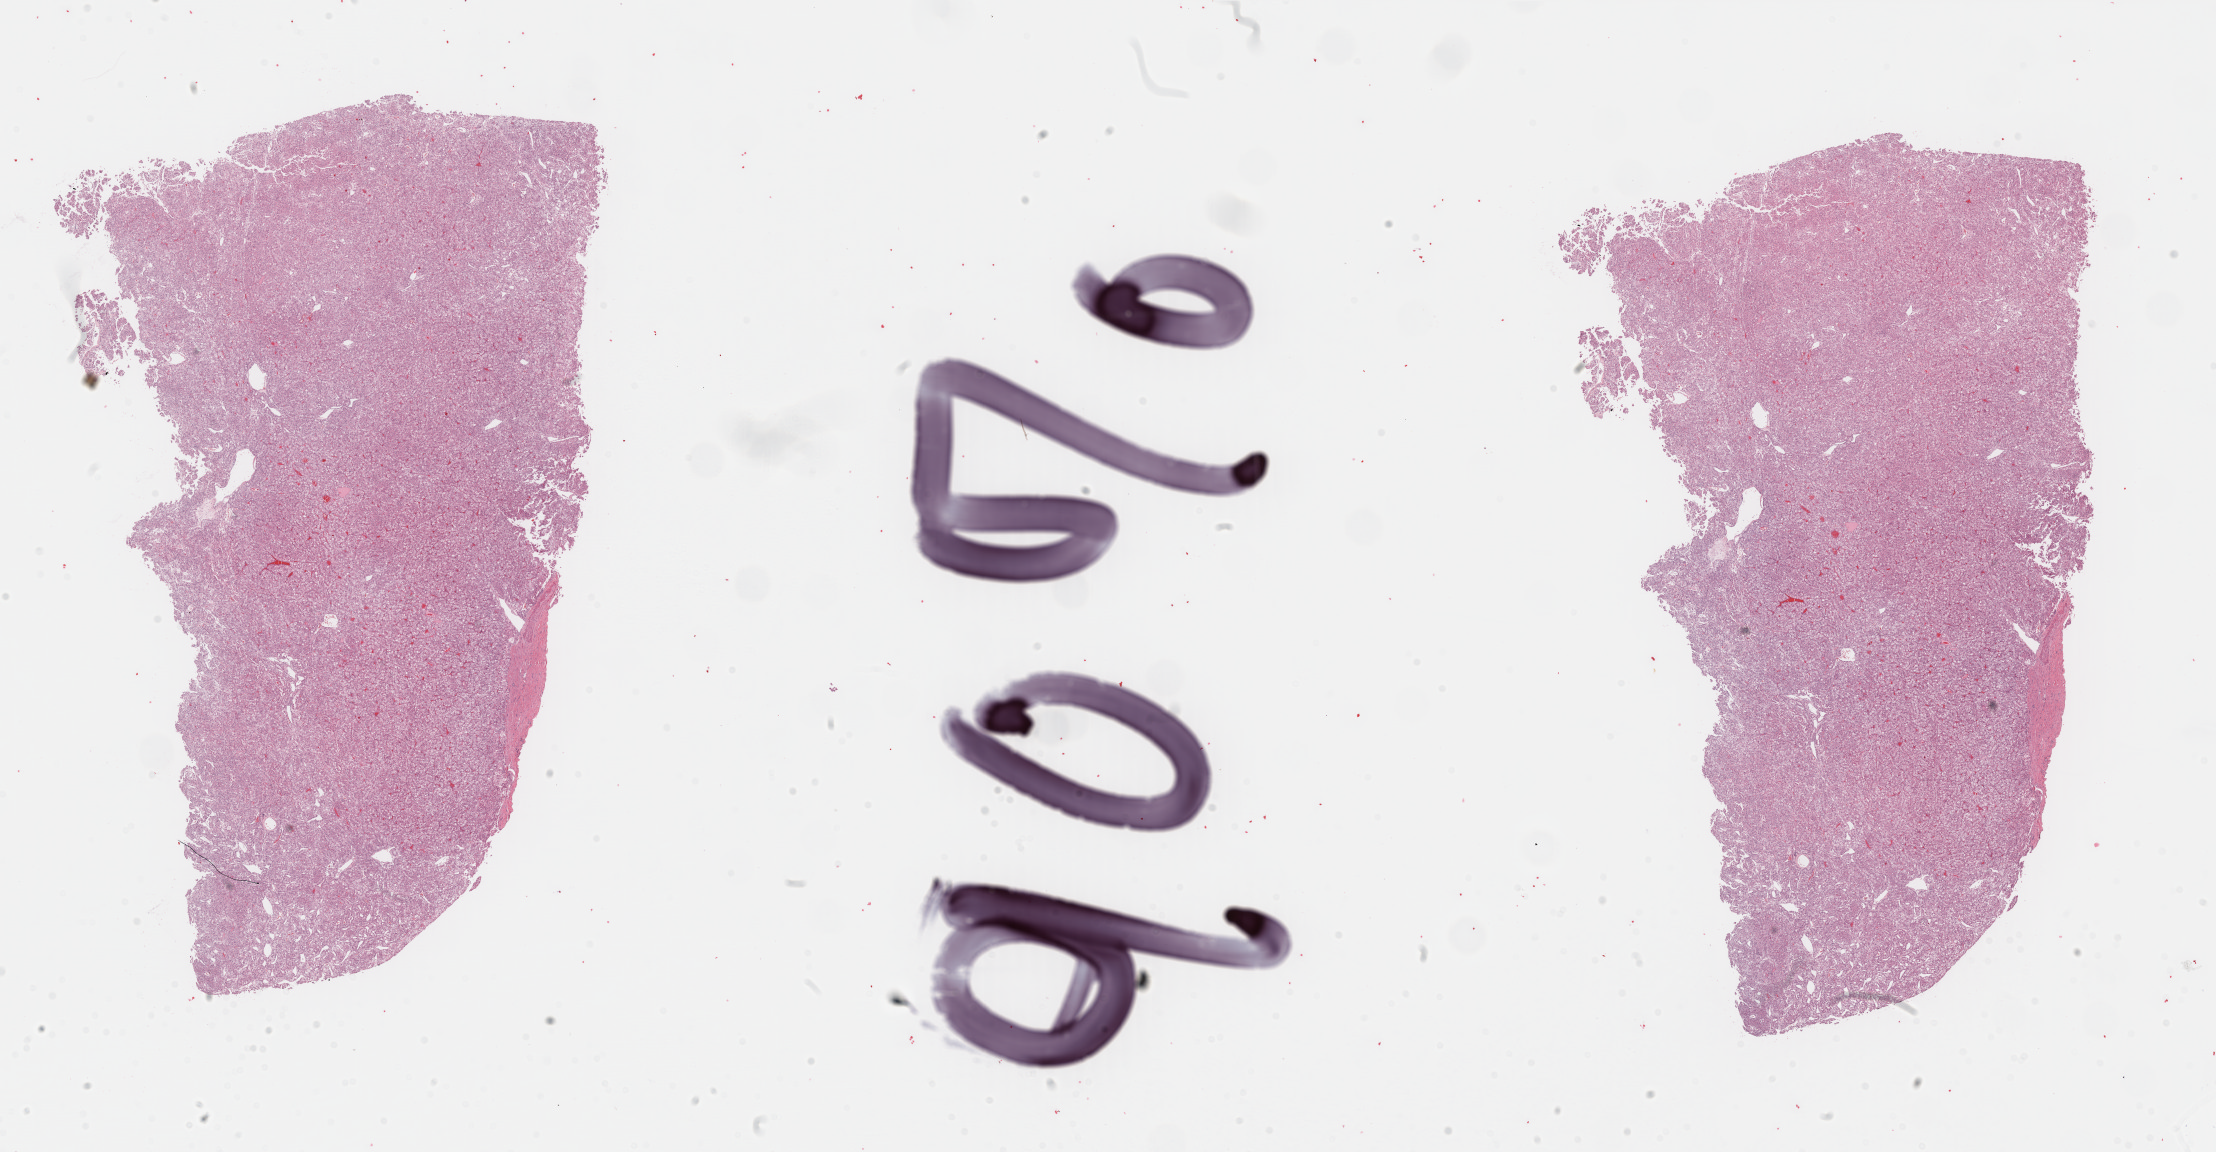
H&E-stained whole-slide image — shown as a low-resolution overview of the whole scanned area (about 35.1 x 18.2 mm, acquisition: 40x scan), formalin-fixed paraffin-embedded (FFPE) diagnostic section, sample: primary tumour, kidney. Patient: male, age at initial diagnosis 38 years.
• laterality: right
• pathologic diagnosis: Renal cell carcinoma, chromophobe type
• AJCC pathologic stage: I (7th edition)